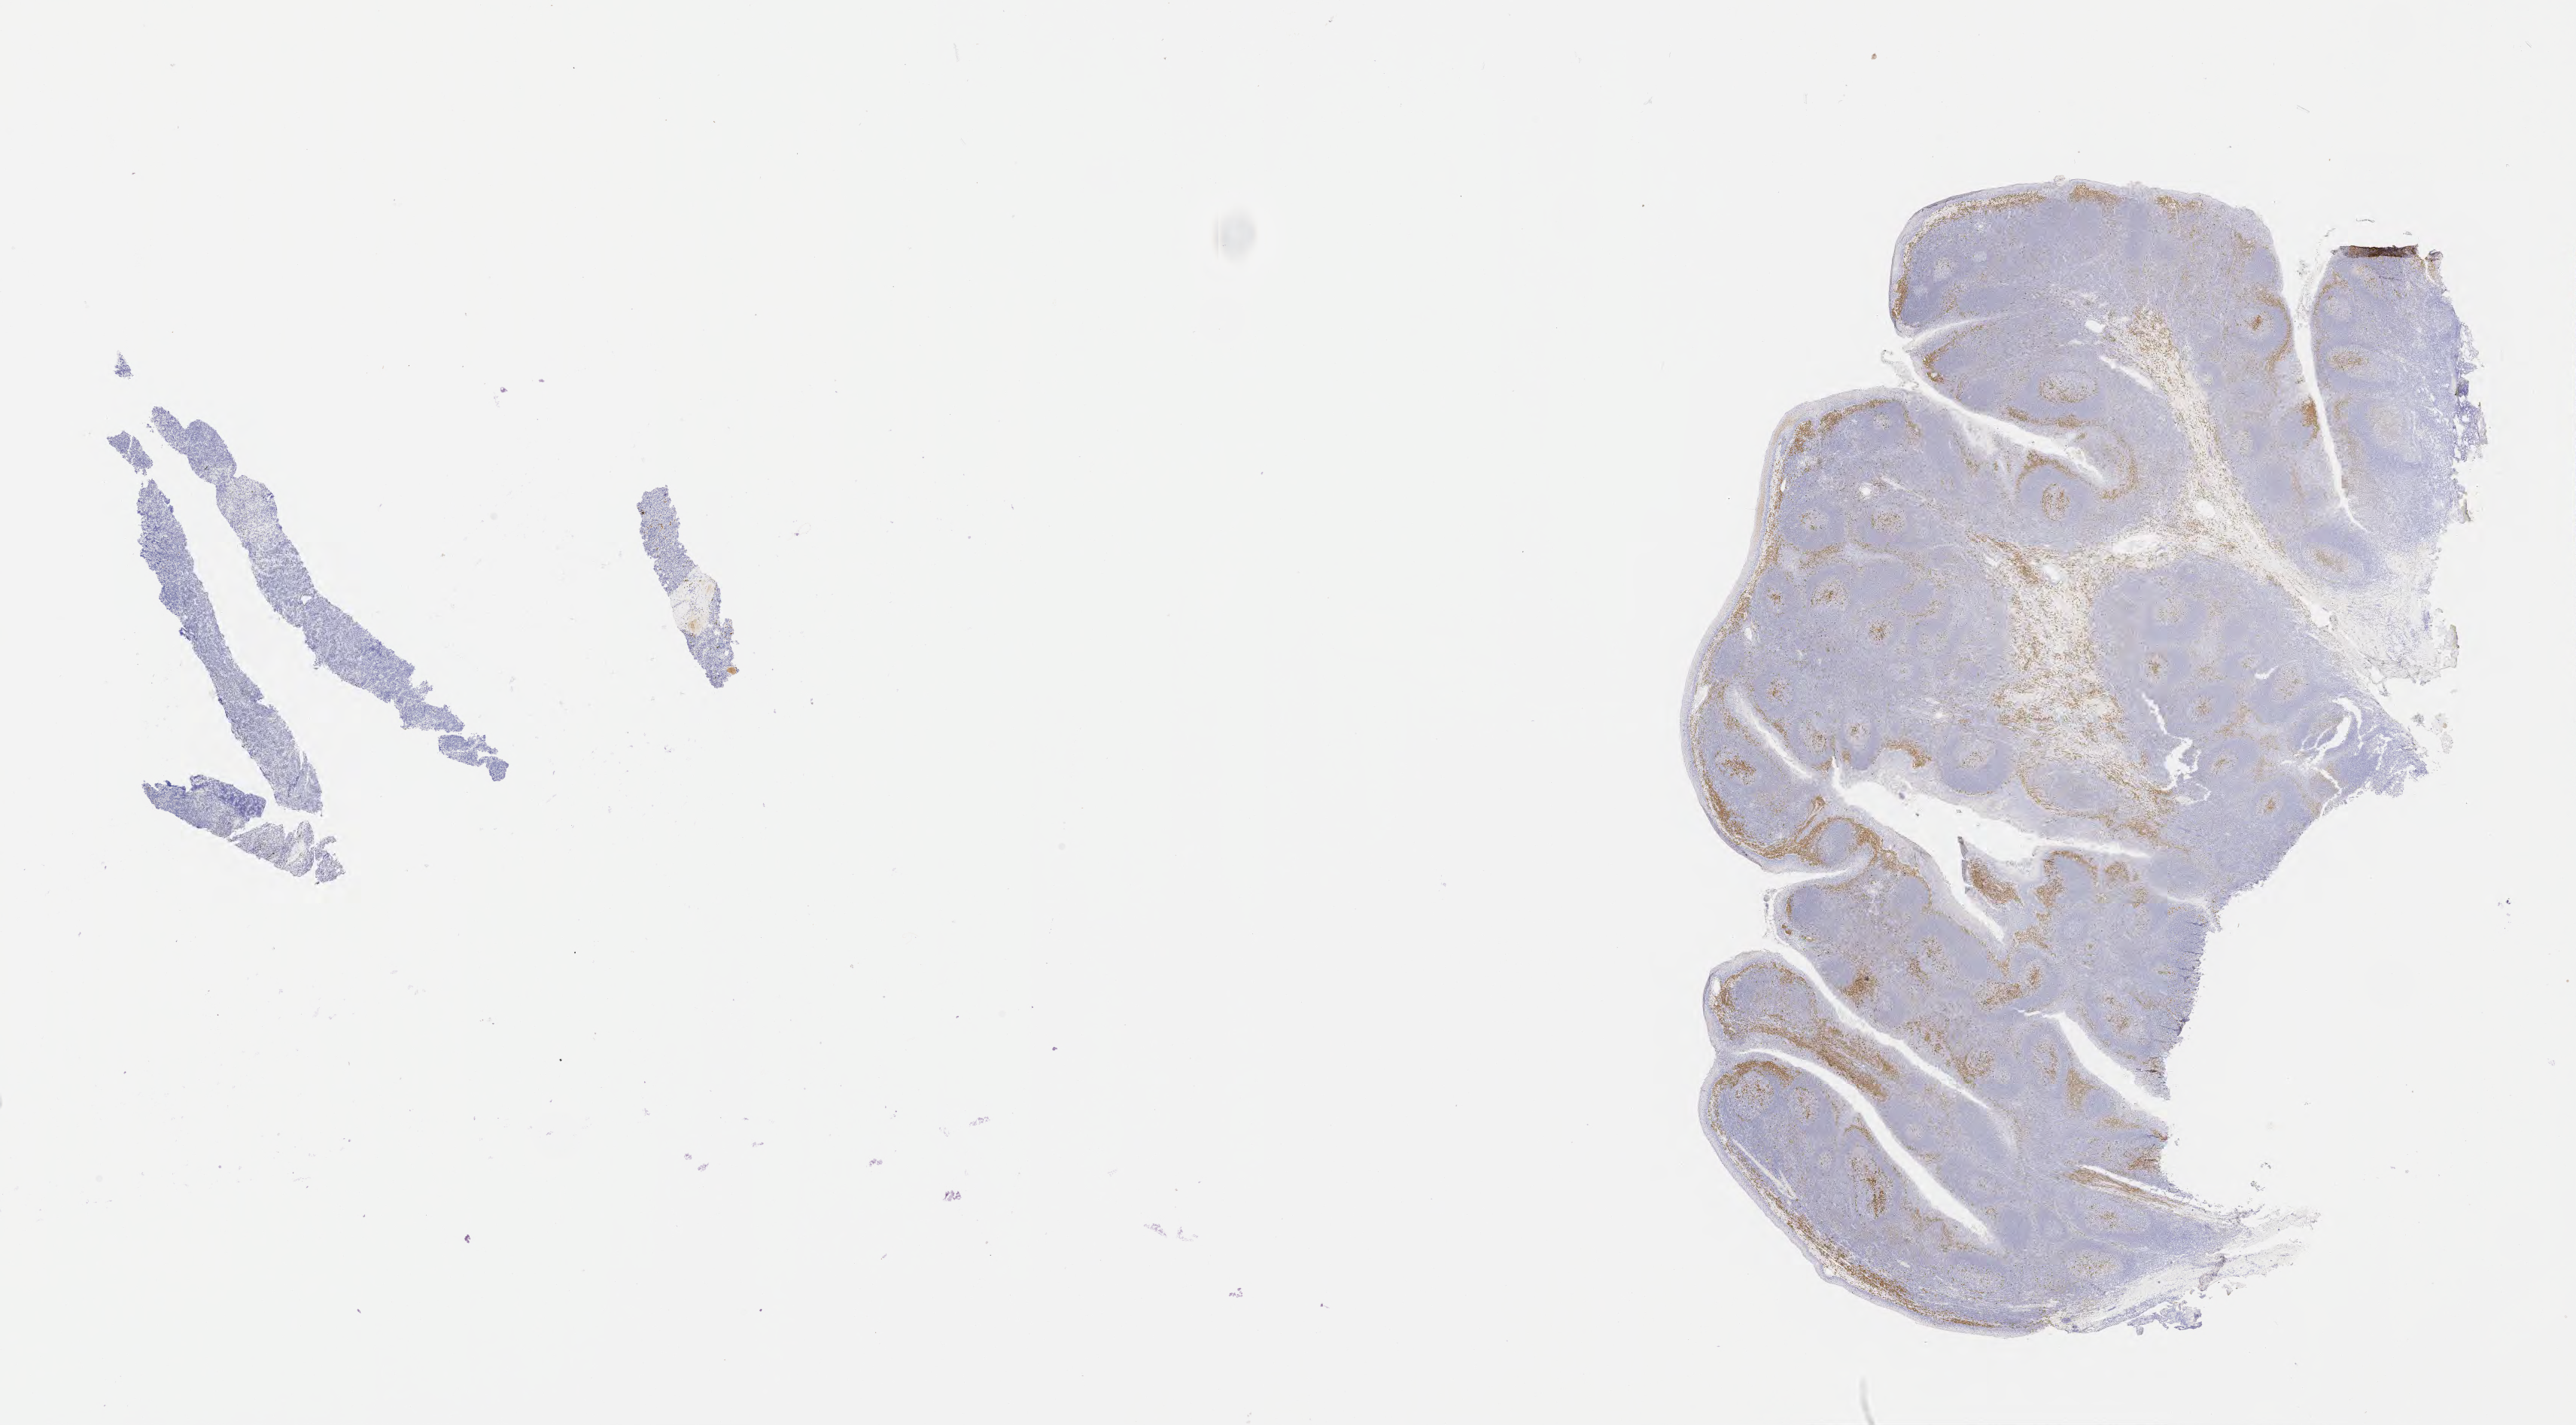
IHC for IRF4/MUM1, whole-slide image, a low-resolution overview of the entire scanned area, about 27.7 x 15.3 mm. Tumor tissue. Male patient, age 13 years.
Histologic diagnosis: Diffuse large B-cell lymphoma, NOS.